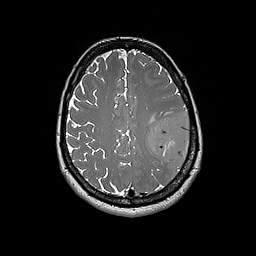
Brain MRI from a brain-tumour surgery series, one axial slice. Slice 68 of 192 in the series (ordered by position). 1 mm slice thickness. 256 × 256 image matrix, field of view 250 × 250 mm. Case-level facts recorded for this patient, not image findings: histopathology: Glioblastoma; WHO grade: 4; IDH mutation: no.
Annotated regions visible in this slice (outlined manually by an expert reader):
- tumour: bounding box (x1, y1, x2, y2) in pixels: (147, 114, 191, 166)